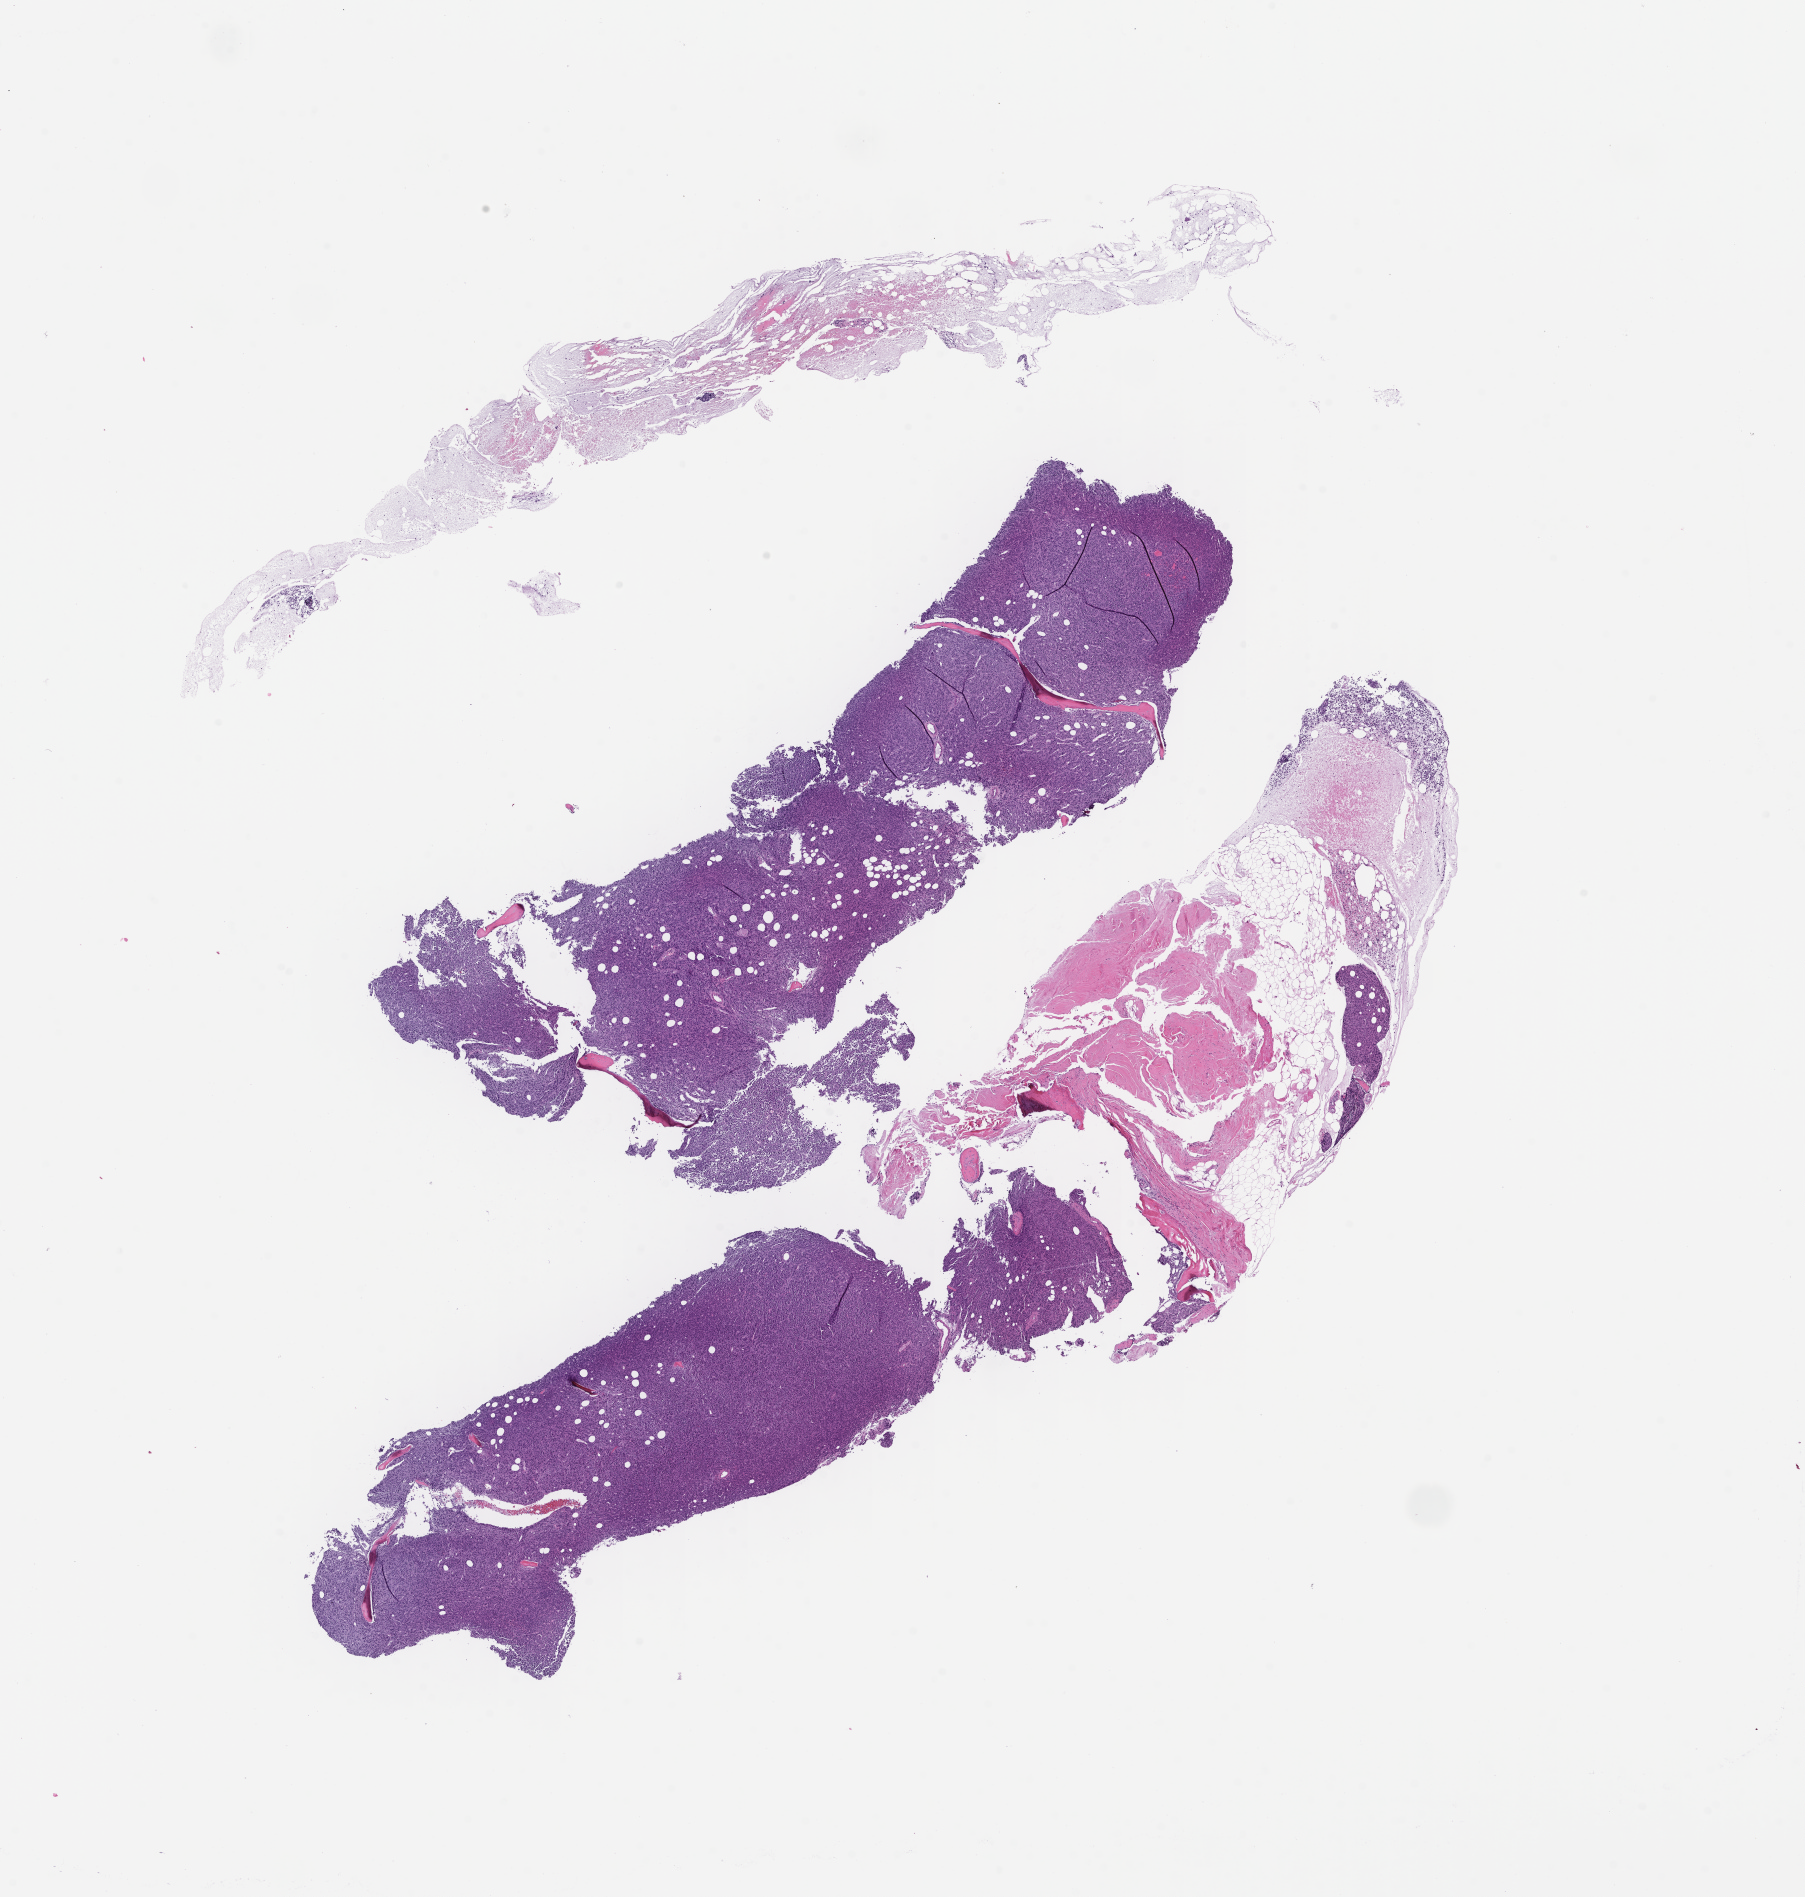
Digitized haematoxylin and eosin-stained section — low-resolution overview of the scanned area, about 14.6 x 15.3 mm, formalin-fixed paraffin-embedded section. Patient sex: female.
This section: metastasis (sampled organ not recorded). Patient diagnosis (primary): Plasma Cell Myeloma.